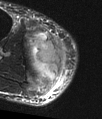
MRI of an extremity soft-tissue mass, one axial slice; position 33 of 48 along the scan axis; T2-weighted fat-saturated; MR volume resampled by the dataset authors to the PET/CT grid (not the native acquisition matrix); 3.27 mm slice thickness; 102 × 119 image matrix. Male patient. Case-level facts recorded for this patient, not image findings: histological type: pleiomorphic liposarcoma; grade: high; site of the primary tumour: right calf.
Outlined on this slice (expert contour drawn on MRI and transferred to this co-registered scan by the dataset authors):
- gross tumour volume including surrounding oedema: bounding box <26,32,70,81> (left, top, right, bottom; pixels)
- gross tumour volume (mass): <35,40,70,75>